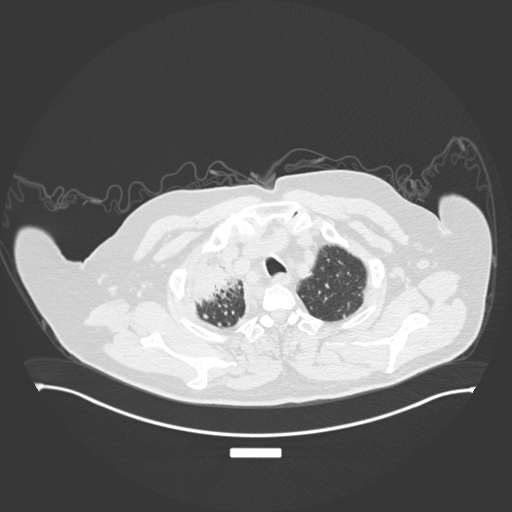
Chest CT, one axial slice. Position 169 of 201 along the scan axis. Reconstruction kernel B30f. Lung window (W 1500 / L -600 HU). 512 × 512 image matrix, field of view 500 × 500 mm. Male patient, age 69 years. Case-level facts recorded for this patient, not image findings: clinical TNM (as recorded): T4 N3 M1.
Outlined on this slice (bounding box drawn by a radiologist):
- lung tumour (recorded histology: adenocarcinoma): bounding box <188,262,244,303> (left, top, right, bottom; pixels)